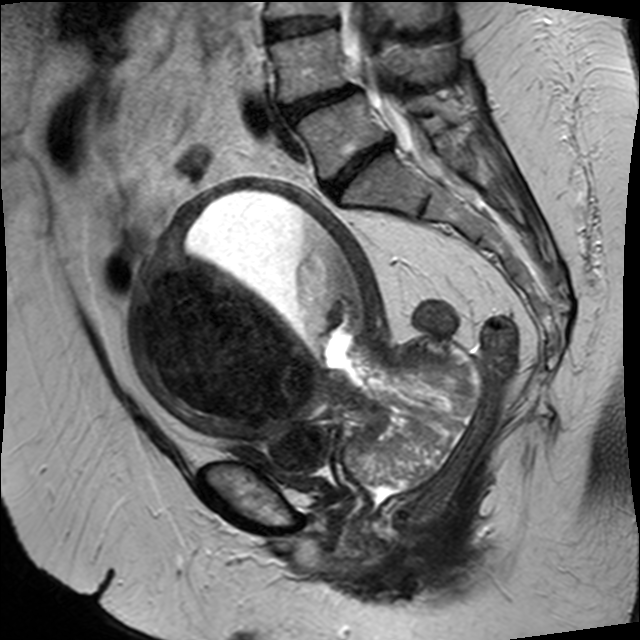
Pelvic MRI for cervical cancer, one sagittal slice. Slice 19 of 34 in the series (ordered by position). T2-weighted. 1.5 T. TE 89 ms, TR 3320 ms. 640 × 640 image matrix. Female patient, age 50 years.
Structures marked on this image (manually delineated by an expert):
- uterus and cervix: bounding box (x1, y1, x2, y2) in pixels: (131, 179, 478, 492)